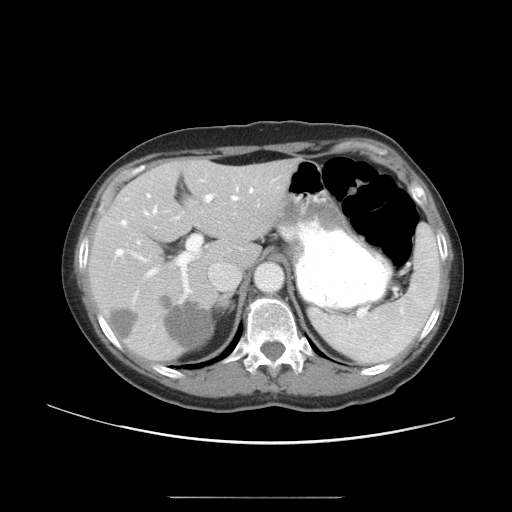
Contrast-enhanced abdominal CT, one axial slice; position 32 of 50 along the scan axis; 120 kVp; soft-tissue window (W 400 / L 40 HU); 5 mm slice thickness; 512 × 512 image matrix, field of view 389 × 389 mm. Female patient, age 58 years. Case-level facts recorded for this patient, not image findings: diagnosis: colorectal cancer liver metastases, imaged before liver resection; multiple liver metastases: yes; largest metastasis: 7.3 cm.
Structures marked on this image (expert manual segmentation):
- hepatic veins: box from (x=116, y=188) to (x=253, y=255) px
- liver: (x=92, y=163)–(x=288, y=360)
- planned liver remnant (the part of the liver to remain after resection): (x=171, y=163)–(x=288, y=264)
- portal vein (with intrahepatic branches): (x=136, y=193)–(x=260, y=295)
- liver metastasis: (x=164, y=299)–(x=210, y=349)
- liver metastasis: (x=112, y=310)–(x=139, y=337)